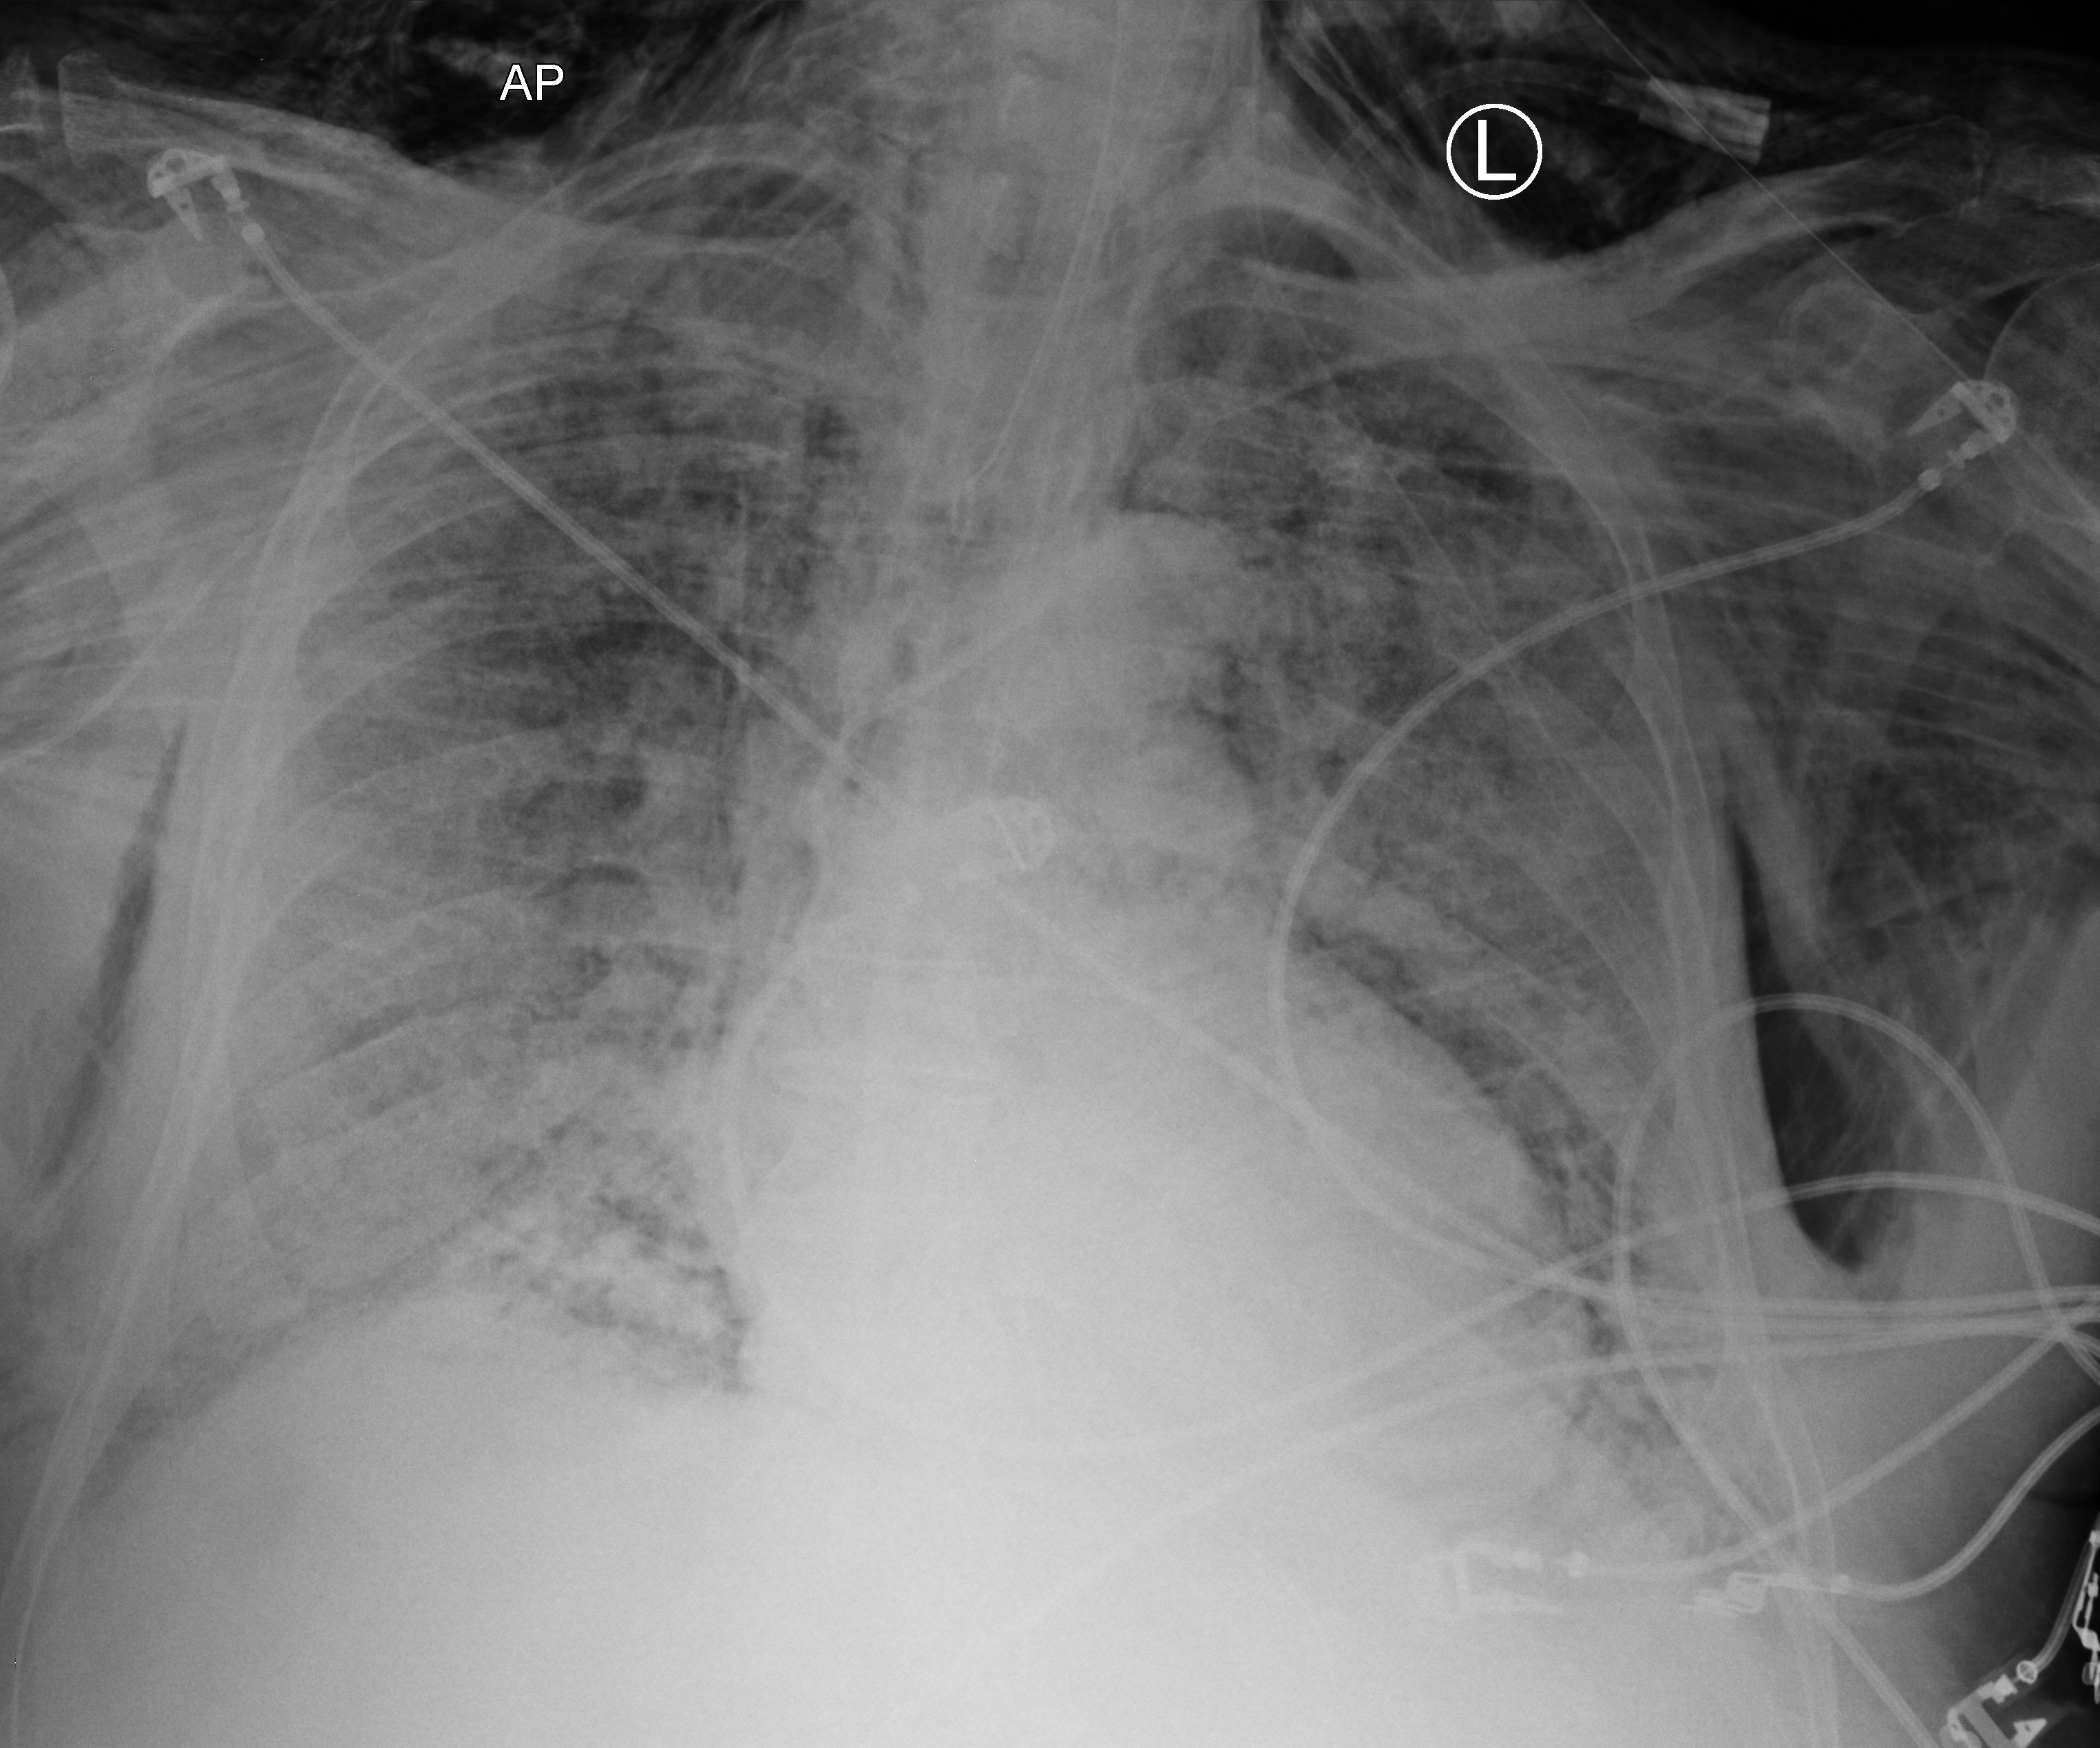
Chest X-ray (portable); anteroposterior (AP) projection. Patient hospitalised with COVID-19; male, aged 75–90 years.
Hospital-stay facts (about this admission, not read from this image; timing relative to this image not recorded):
- length of hospital stay: 14 days